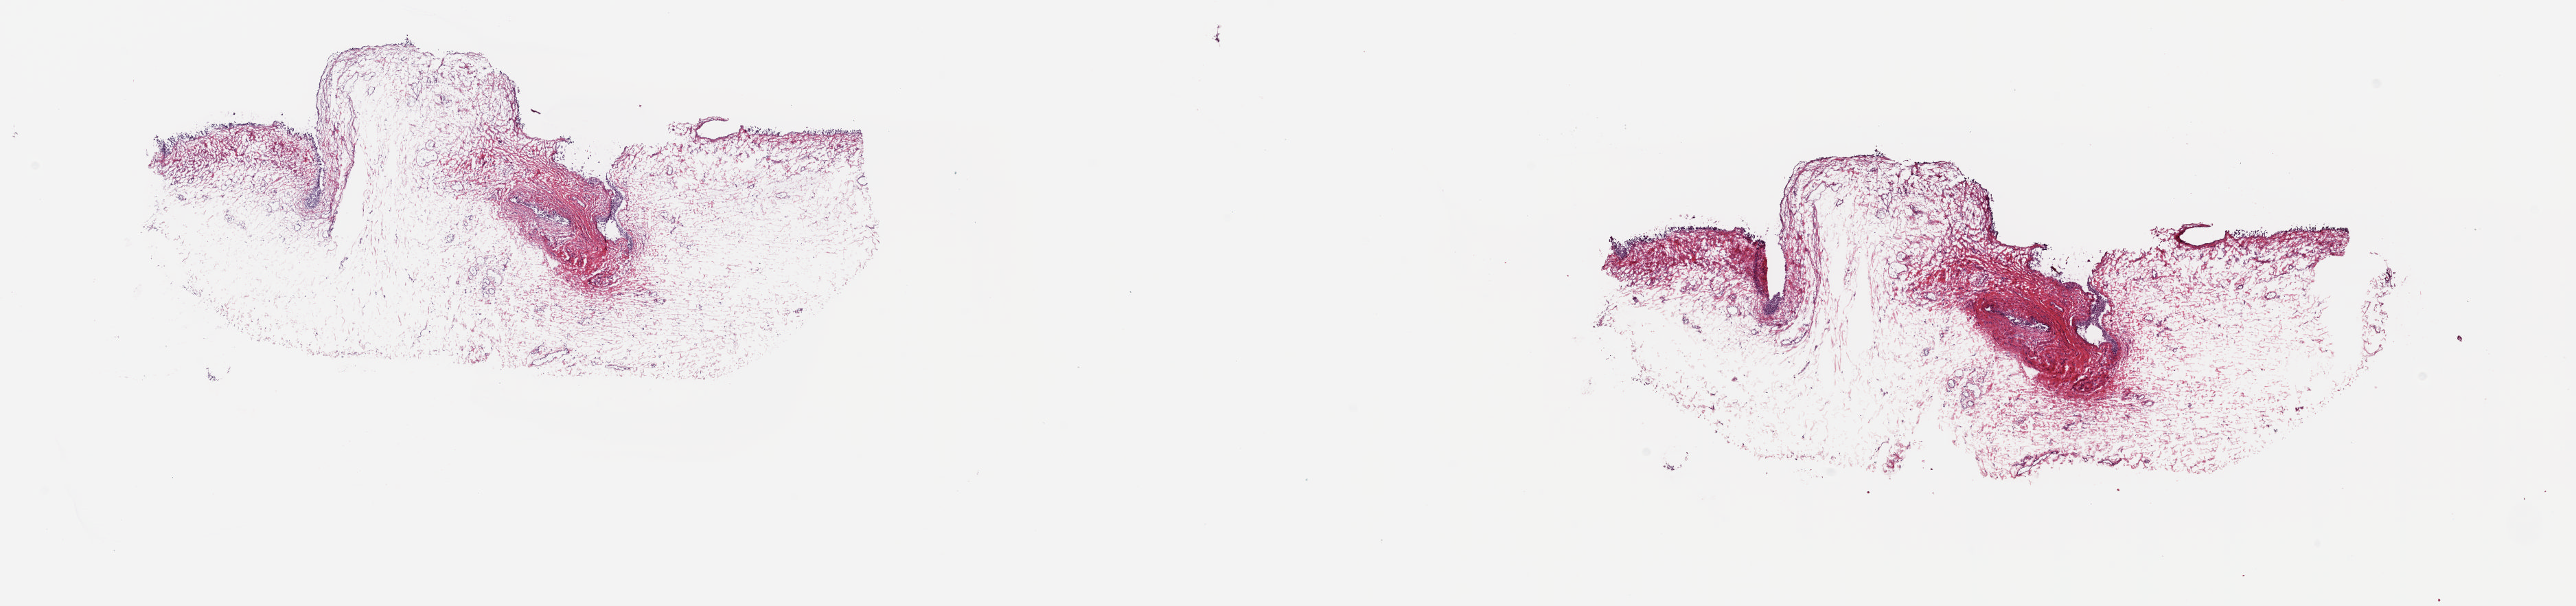
Digitized Hematoxylin and eosin (H&E) stained tissue section (whole slide), shown as a low-resolution overview of the whole scanned area (about 29.8 x 7.0 mm, acquisition: 20x scan), frozen section from the top of the tissue portion, sample: solid tissue normal (non-tumour tissue), bladder. Patient: male, age at initial diagnosis 70 years. Composition of this section per pathologist review: tumour cells 0%, tumour nuclei 0%, normal cells 100%, stromal cells 0%, necrosis 0%. Infiltration values recorded for this section: lymphocyte infiltration 0%, monocyte infiltration 0%, neutrophil infiltration 0%.
* this section: solid tissue normal sample (biorepository sample class)
* patient diagnosis: Transitional cell carcinoma